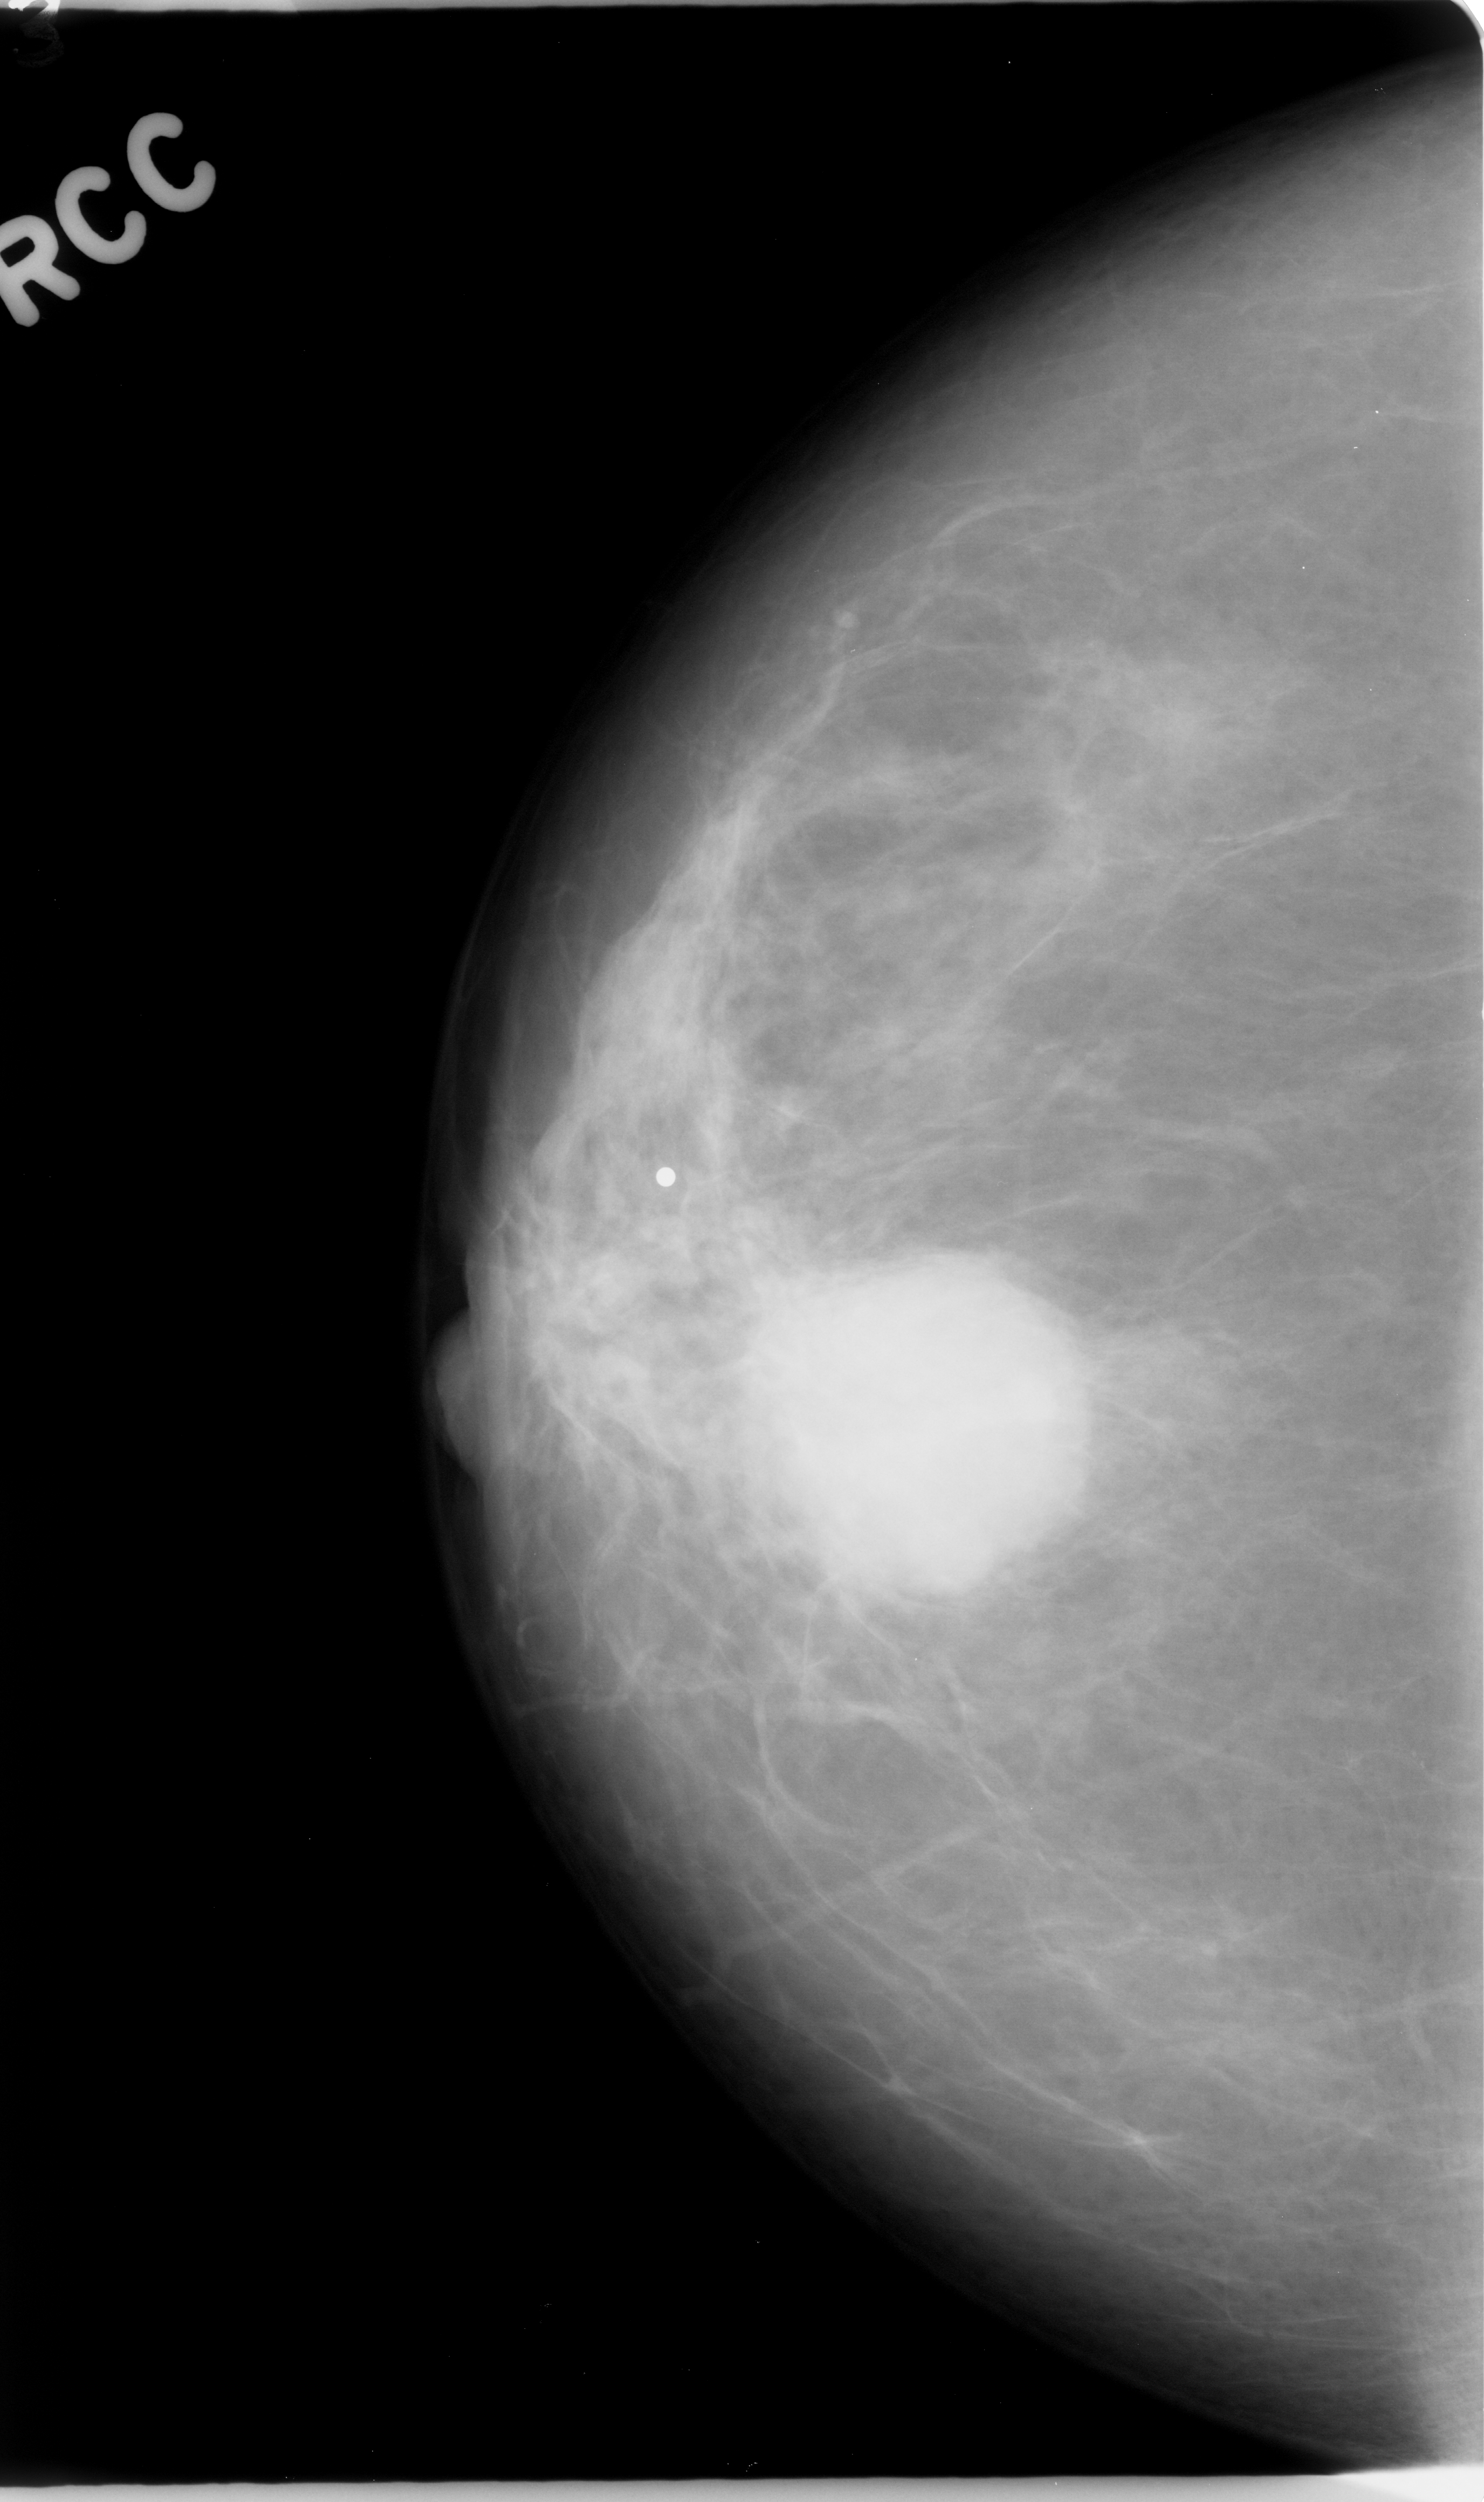
Scanned film-screen mammogram. Right breast. Craniocaudal (CC) view. Breast composition: almost entirely fatty (BI-RADS density category 1 of 4). 1484 × 2502 image matrix.
Expert-marked regions of interest on this image (one box per marked abnormality):
- mass, shape lobulated, margins microlobulated; BI-RADS assessment category 5; pathology (as recorded): malignant: bounding box <738,1235,1110,1602> (left, top, right, bottom; pixels)